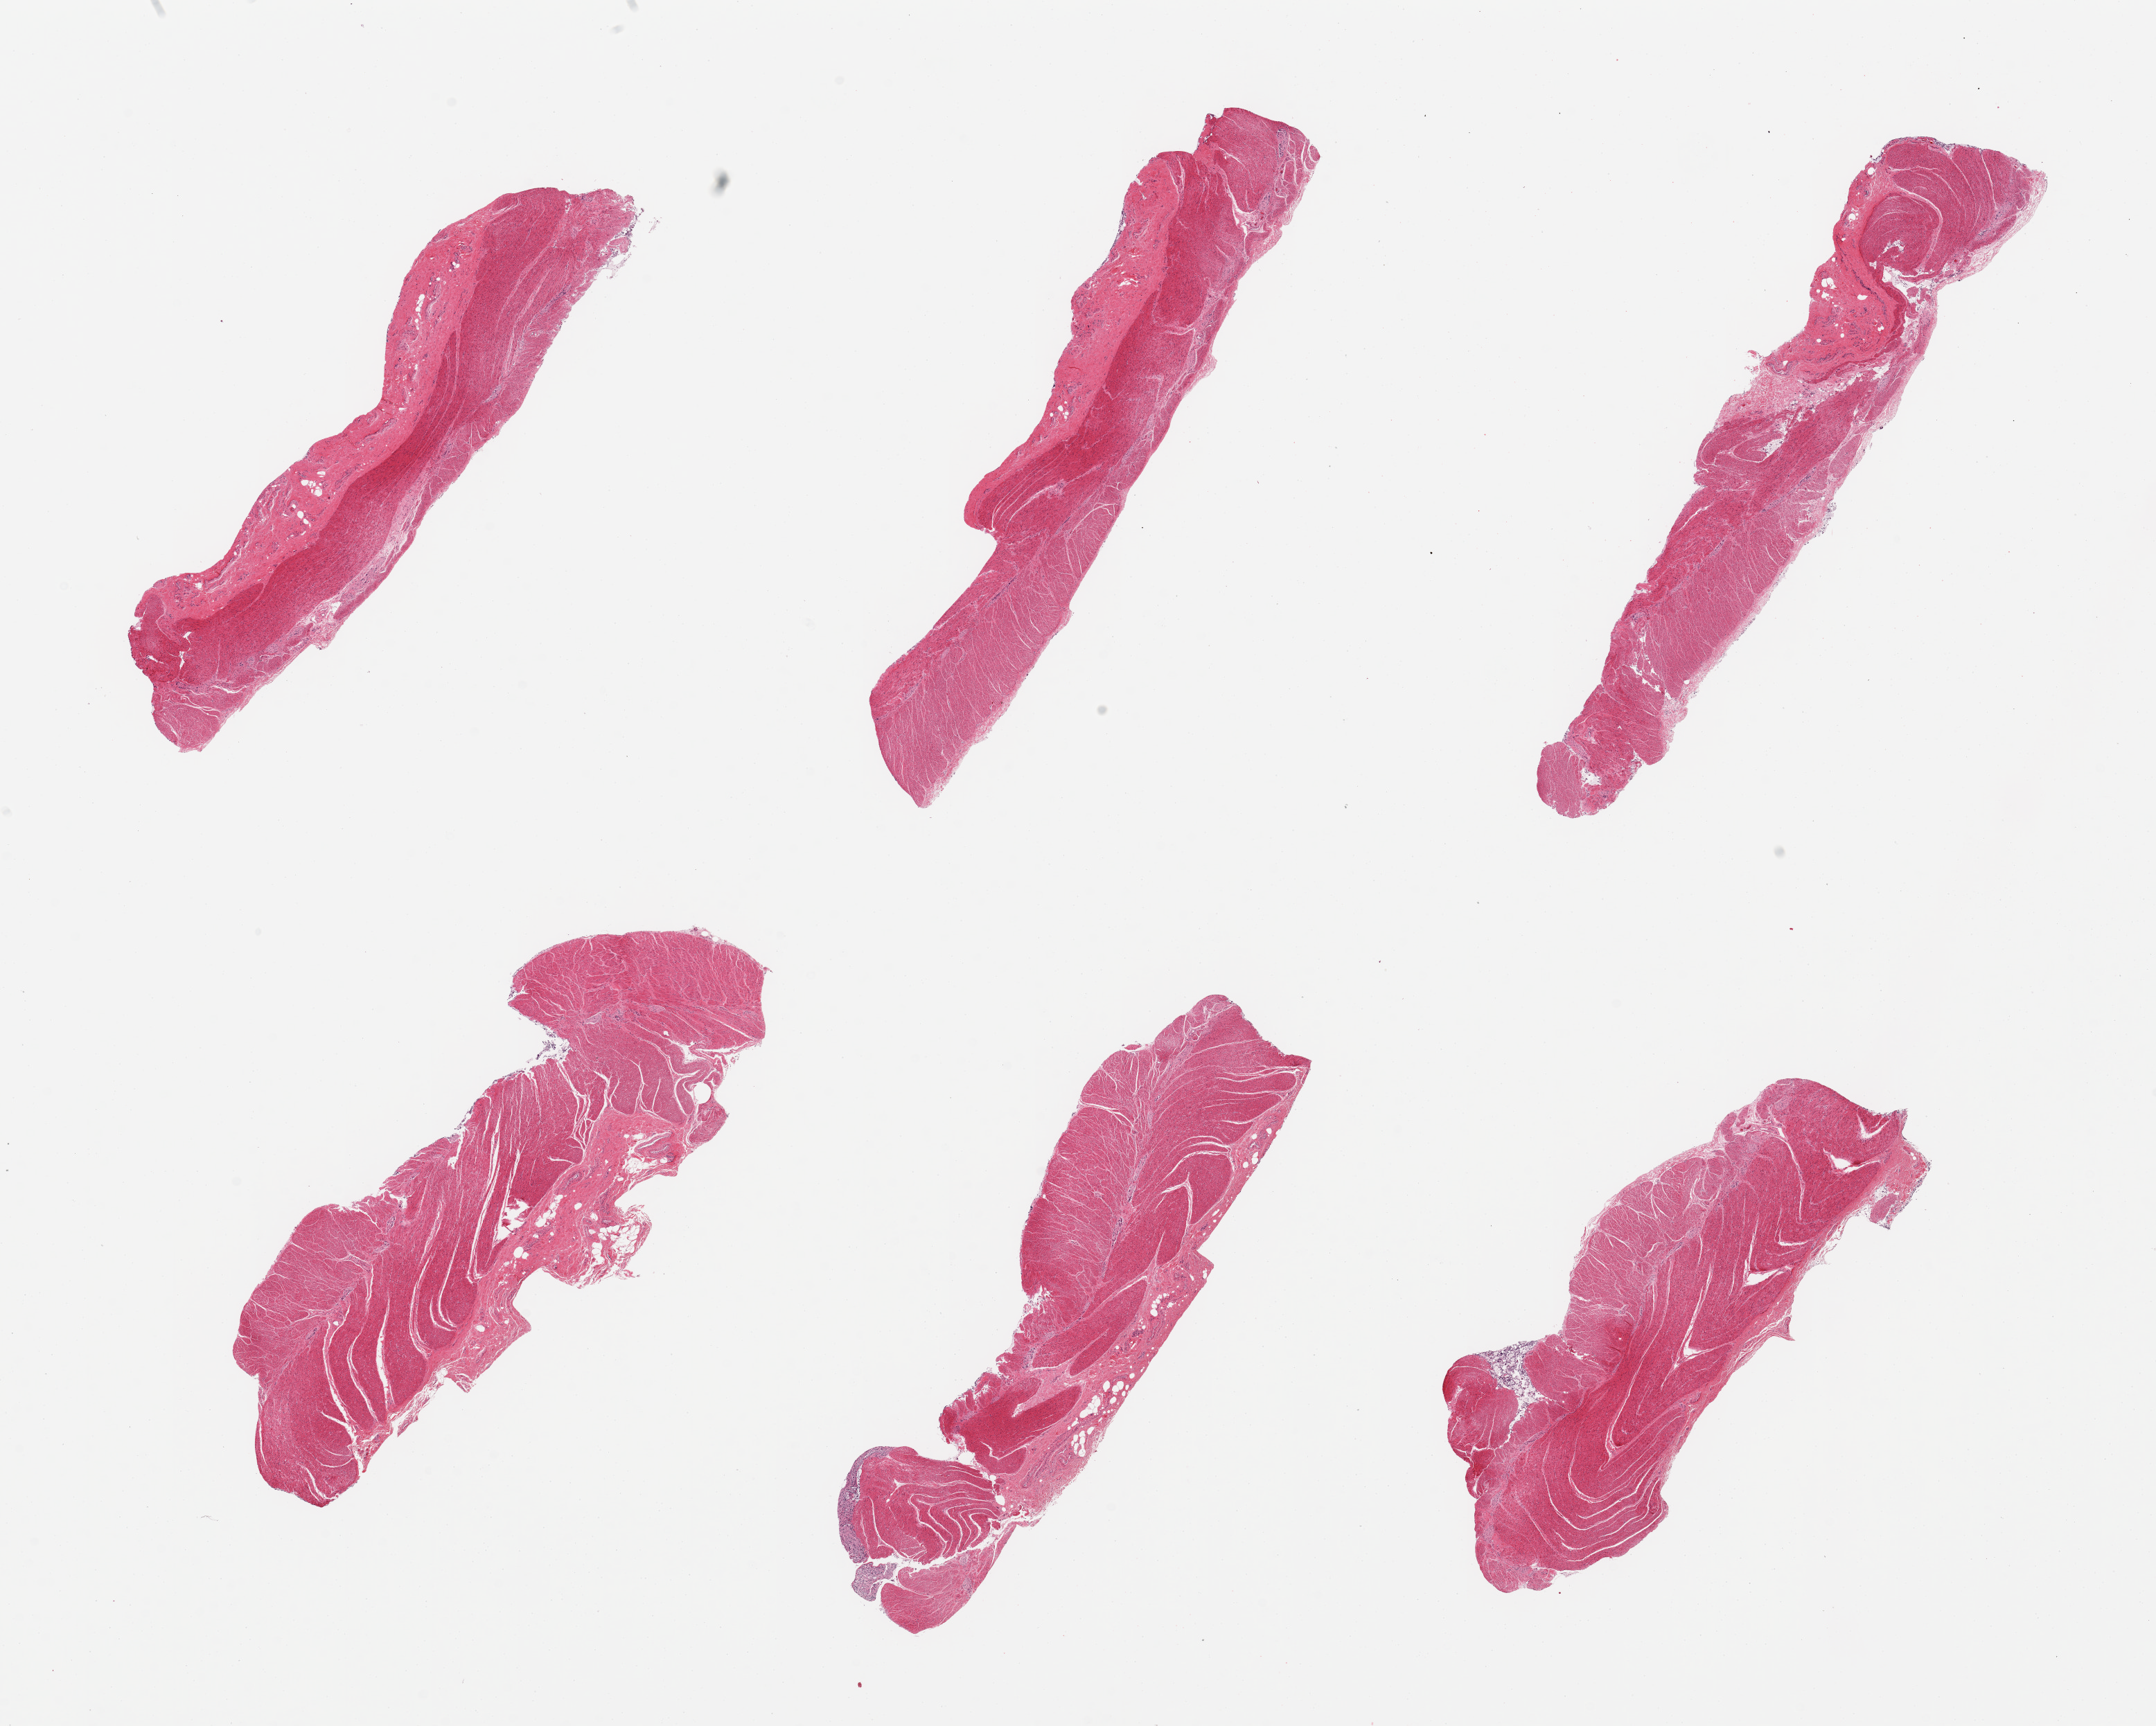
Digitized haematoxylin and eosin-stained section, low-resolution overview of the scanned area, about 24.6 x 19.7 mm (slide scanned at 20x). PAXgene-fixed paraffin-embedded (PFPE) section. Section of sigmoid colon (target tissue). Tissue donor sample. Donor: male.
Reviewer comment on this tissue sample: 6 pieces, few small foci of detached and autolyzed mucosal tissue.